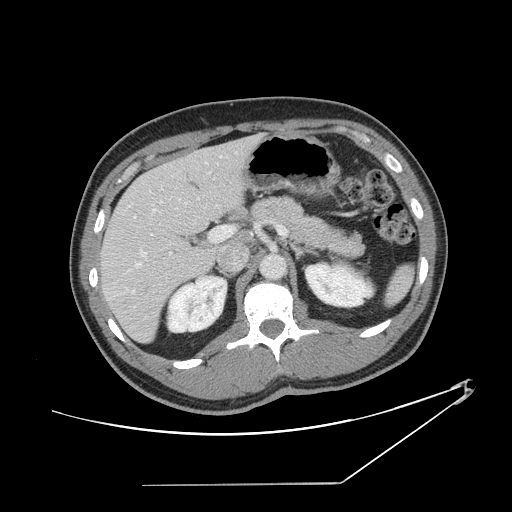
Contrast-enhanced abdominal CT, one axial slice. Slice 81 of 152 in the series (ordered by position). Intravenous contrast given. Soft-tissue window (W 400 / L 40 HU). 2.5 mm slice thickness. 512 × 512 image matrix. Male patient, age 45 years. Case-level facts recorded for this patient, not image findings: diagnosis: colorectal cancer liver metastases, imaged before liver resection; multiple liver metastases: no; largest metastasis: 1 cm.
Outlined on this slice (outlined manually by an expert reader):
- hepatic veins: bounding box (x1, y1, x2, y2) in pixels: (111, 155, 223, 293)
- liver: (102, 137, 257, 341)
- planned liver remnant (the part of the liver to remain after resection): (102, 156, 216, 341)
- portal vein (with intrahepatic branches): (135, 225, 286, 267)